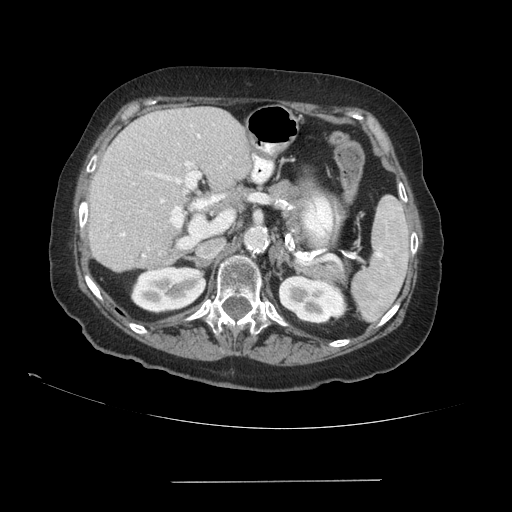
Contrast-enhanced abdominal CT (liver protocol), one axial slice; slice 55 of 89 in the series (ordered by position); soft-tissue window (W 400 / L 40 HU); 2.5 mm slice thickness; 512 × 512 image matrix. From the clinical record (not read from this slice): diagnosis: hepatocellular carcinoma (patient treated with transarterial chemoembolisation; whether this scan precedes or follows treatment is not stated here); TNM stage (as recorded): Stage-IVA.
Annotated regions visible in this slice (semi-automatic segmentation, software-assisted and operator-edited):
- liver parenchyma outside the tumour (the mass and vessels are separate outlines, so this box may not span the whole liver): box from (x=88, y=106) to (x=251, y=270) px
- liver vessels: (x=120, y=125)–(x=224, y=257)